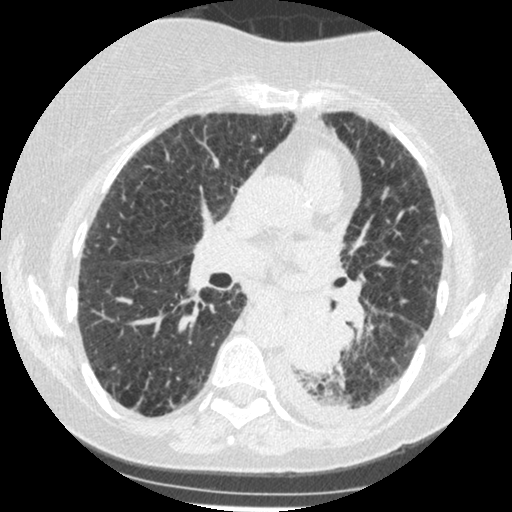
Low-dose screening chest CT, one axial slice; position 134 of 341 along the scan axis; 120 kVp; lung window (W 1500 / L -600 HU); 1.25 mm slice thickness; 512 × 512 image matrix, field of view 310 × 310 mm.
Structures marked on this image (expert manual segmentation):
- lesion 1 (tumor, lower lobe of left lung): bounding box [x1, y1, x2, y2] px = [286, 308, 342, 374]